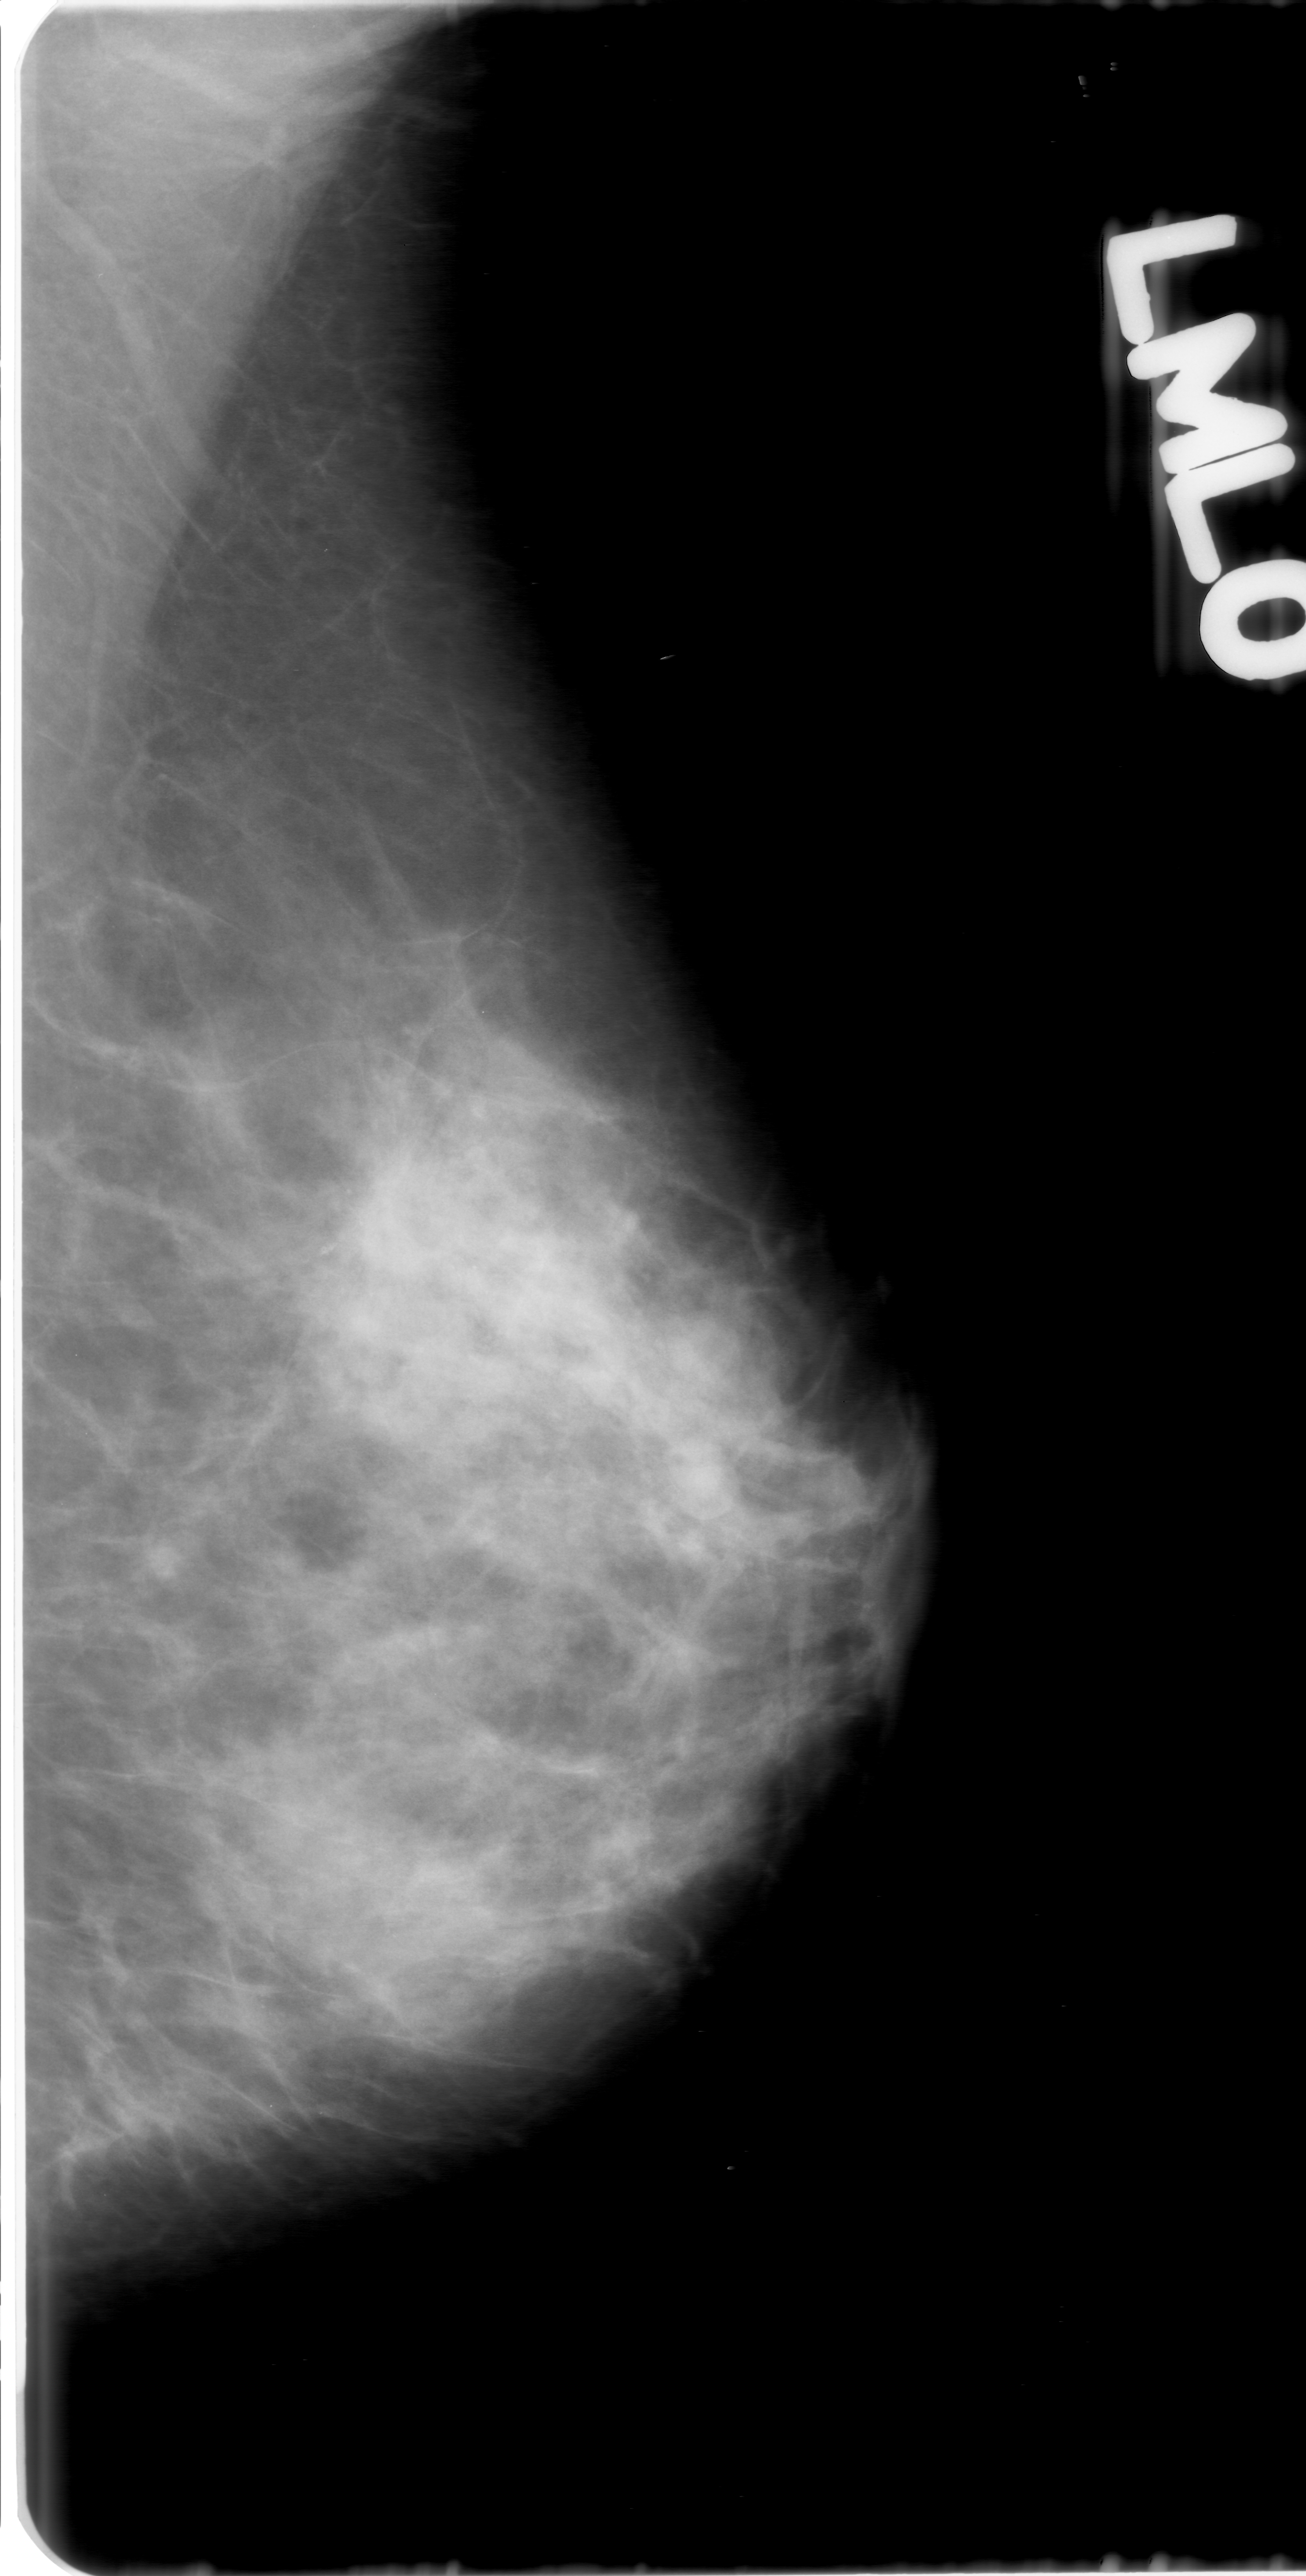
Scanned film-screen mammogram. Left breast. MLO view. BI-RADS breast density category 3 (scale 1–4). 1306 × 2576 image matrix.
Expert-marked regions of interest on this image (one box per marked abnormality):
- calcifications, morphology amorphous, distribution clustered; BI-RADS assessment category 3; subtlety rating 2 on a 1 (subtle) to 5 (obvious) scale; pathology (as recorded): malignant: bounding box <232,1003,622,1381> (left, top, right, bottom; pixels)